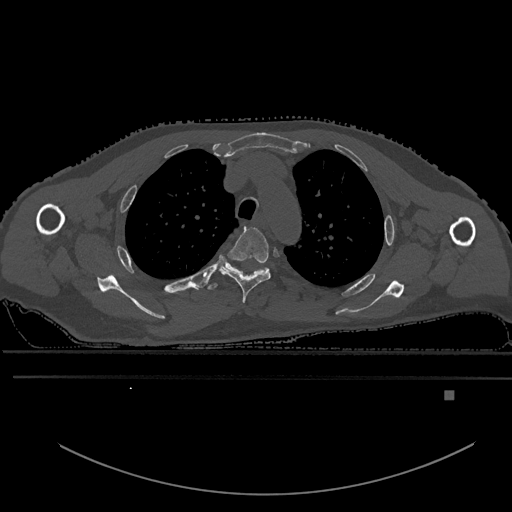
CT including the spine, one axial slice; slice 442 of 969 in the series (ordered by position); bone window (W 1800 / L 400 HU); 512 × 512 image matrix, field of view 456 × 456 mm. Male patient, age 82 years. Case-level facts recorded for this patient, not image findings: primary cancer: prostate; vertebrae with lytic lesions (as recorded): T11, T9, T8, T2.
Annotated regions visible in this slice (semi-automatic segmentation, software-assisted and operator-edited):
- T3 vertebra: box from (x=219, y=227) to (x=272, y=304) px
- T4 vertebra: (x=208, y=261)–(x=269, y=291)